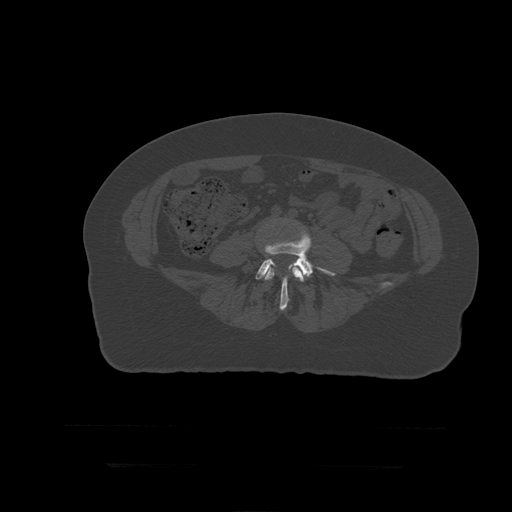
CT including the spine, one axial slice. Slice 82 of 399 in the series (ordered by position). Reconstruction kernel STANDARD. Bone window (W 1800 / L 400 HU). 1.25 mm slice thickness. 512 × 512 image matrix. Patient age 41 years. Case-level facts recorded for this patient, not image findings: primary cancer: breast.
Annotated regions visible in this slice (semi-automatic segmentation, software-assisted and operator-edited):
- L4 vertebra: bounding box <265,262,304,297> (left, top, right, bottom; pixels)
- L5 vertebra: <256,234,336,311>